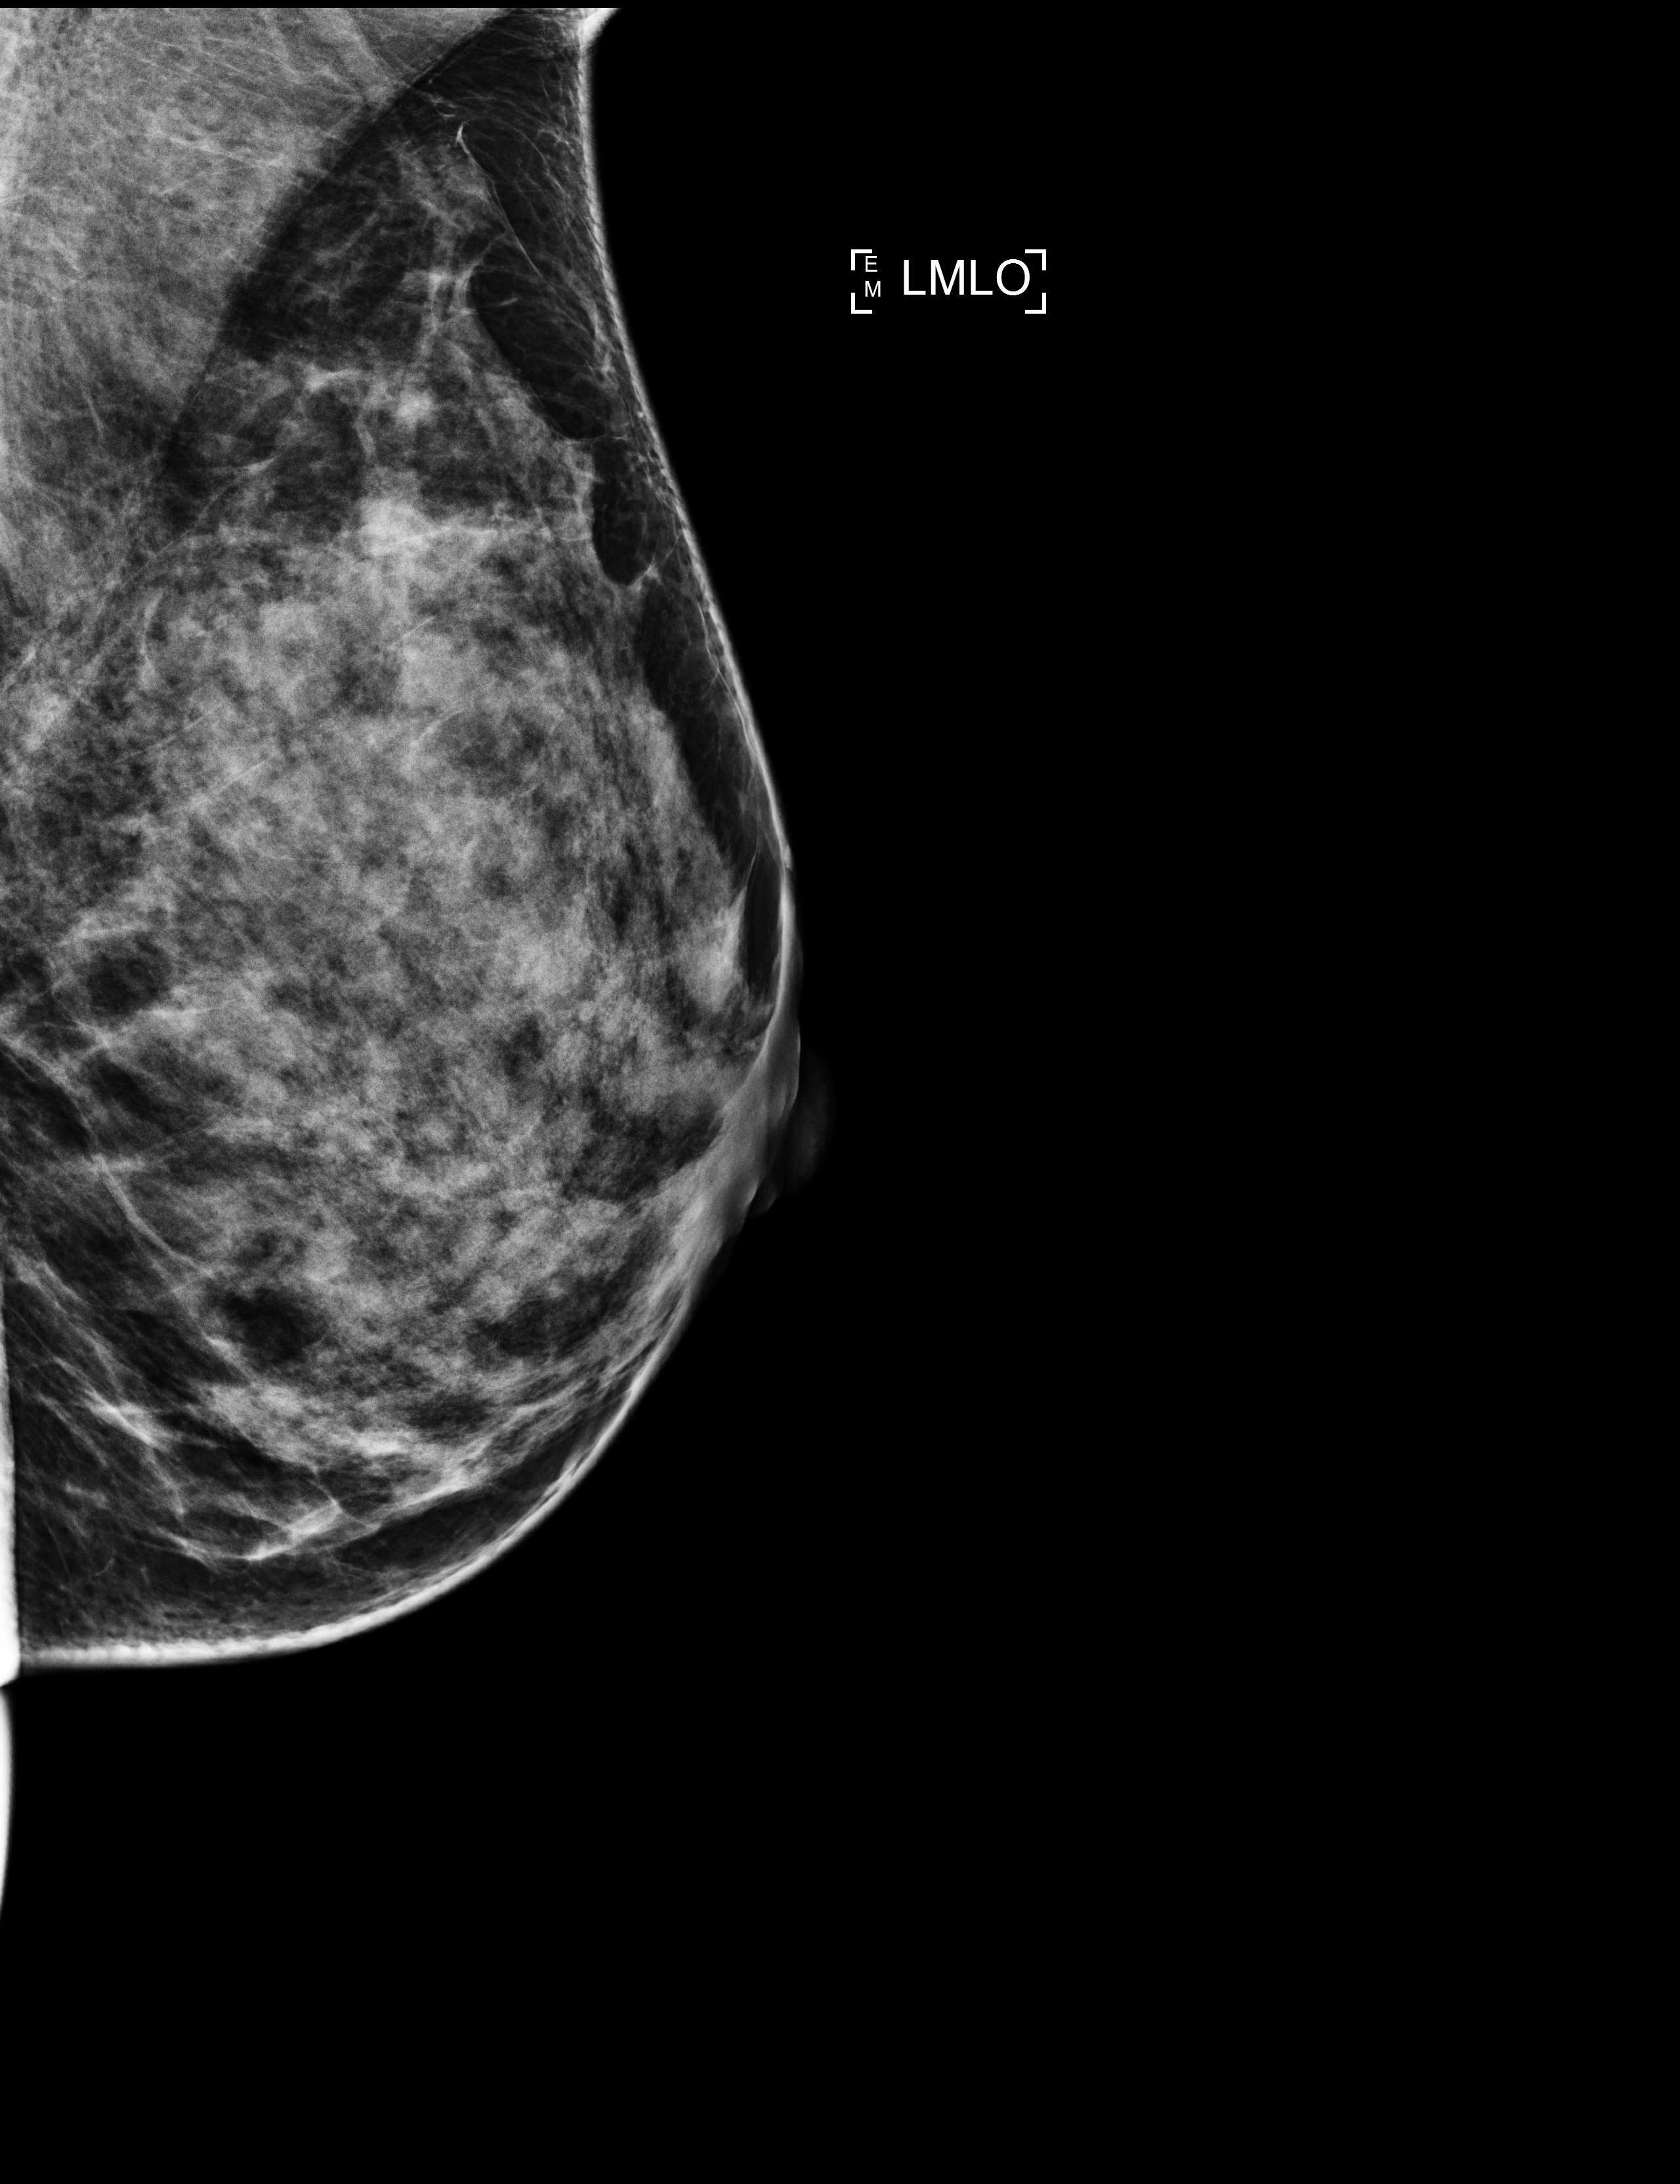
Annual screening mammography examination; compressed breast thickness 55 mm. Patient aged 44 years (female).
Image type: full-field digital mammogram. Breast: left. Projection: MLO view.